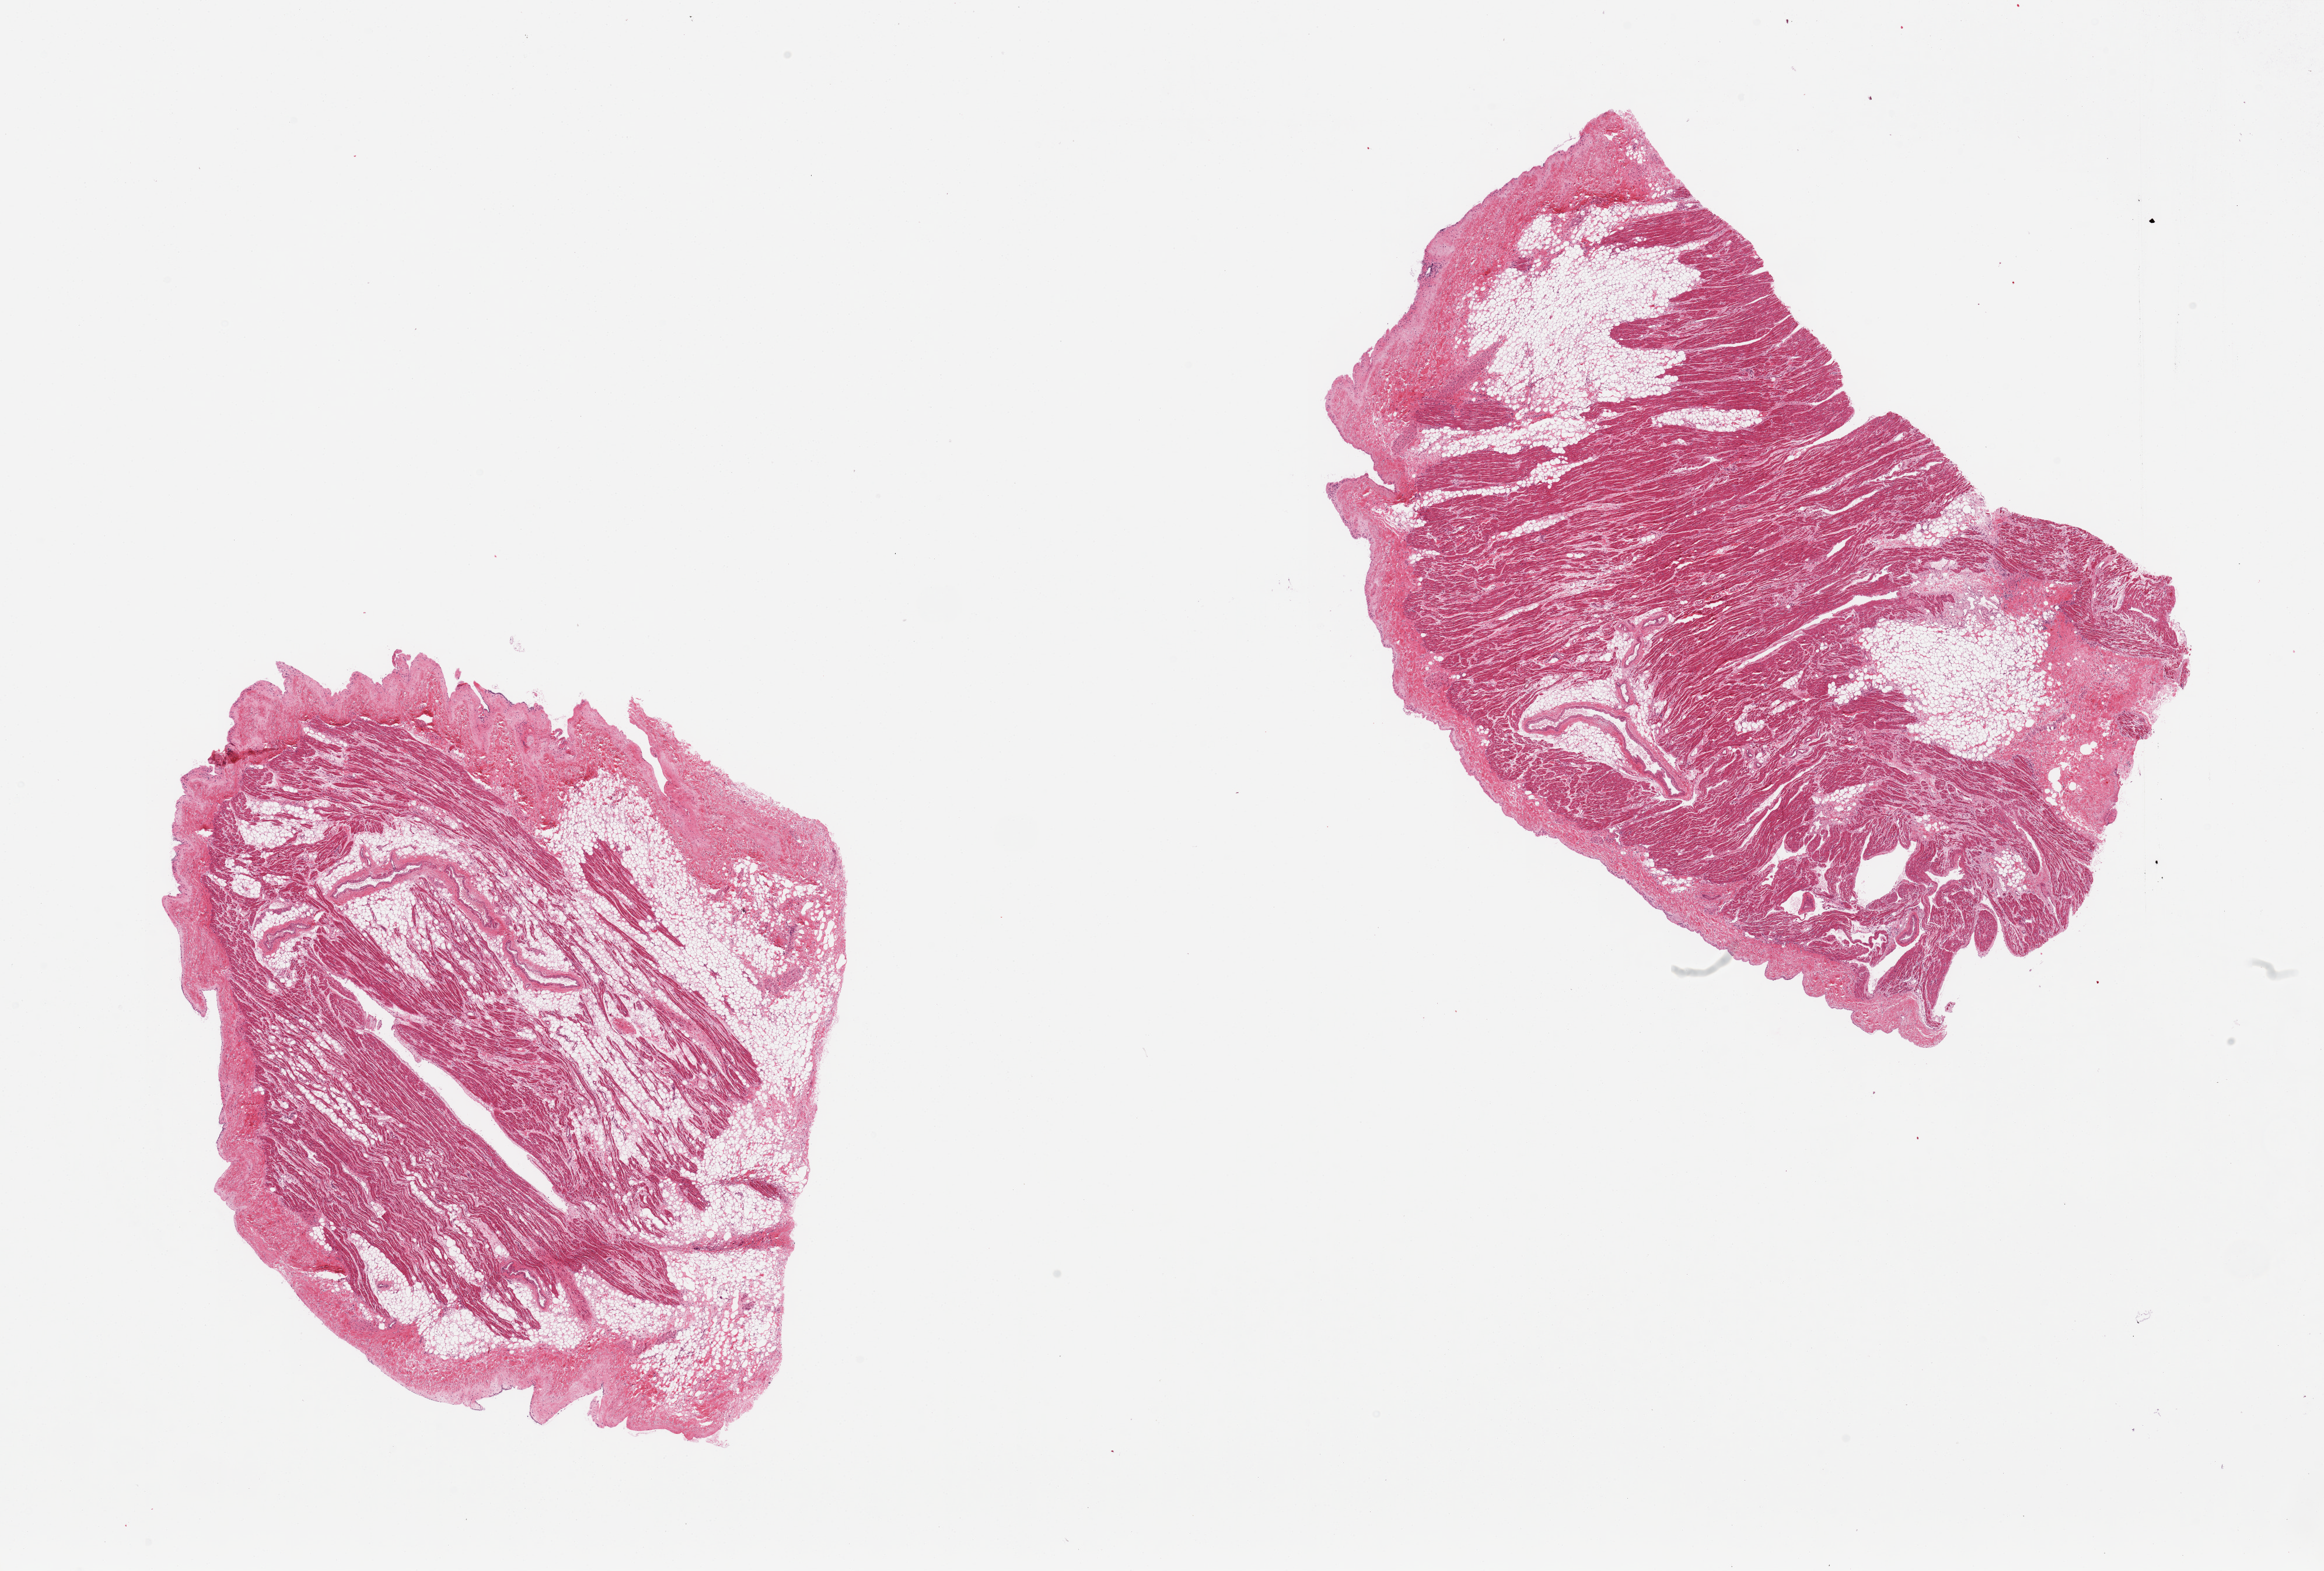
Haematoxylin and eosin whole-slide image, brightfield — low-resolution overview of the scanned area, about 31.5 x 21.3 mm. PAXgene-fixed paraffin-embedded (PFPE) section. Section of auricular appendage (target tissue). Donor tissue sample.
Review note (as recorded): 2 pieces, ~40% interstitial fat.